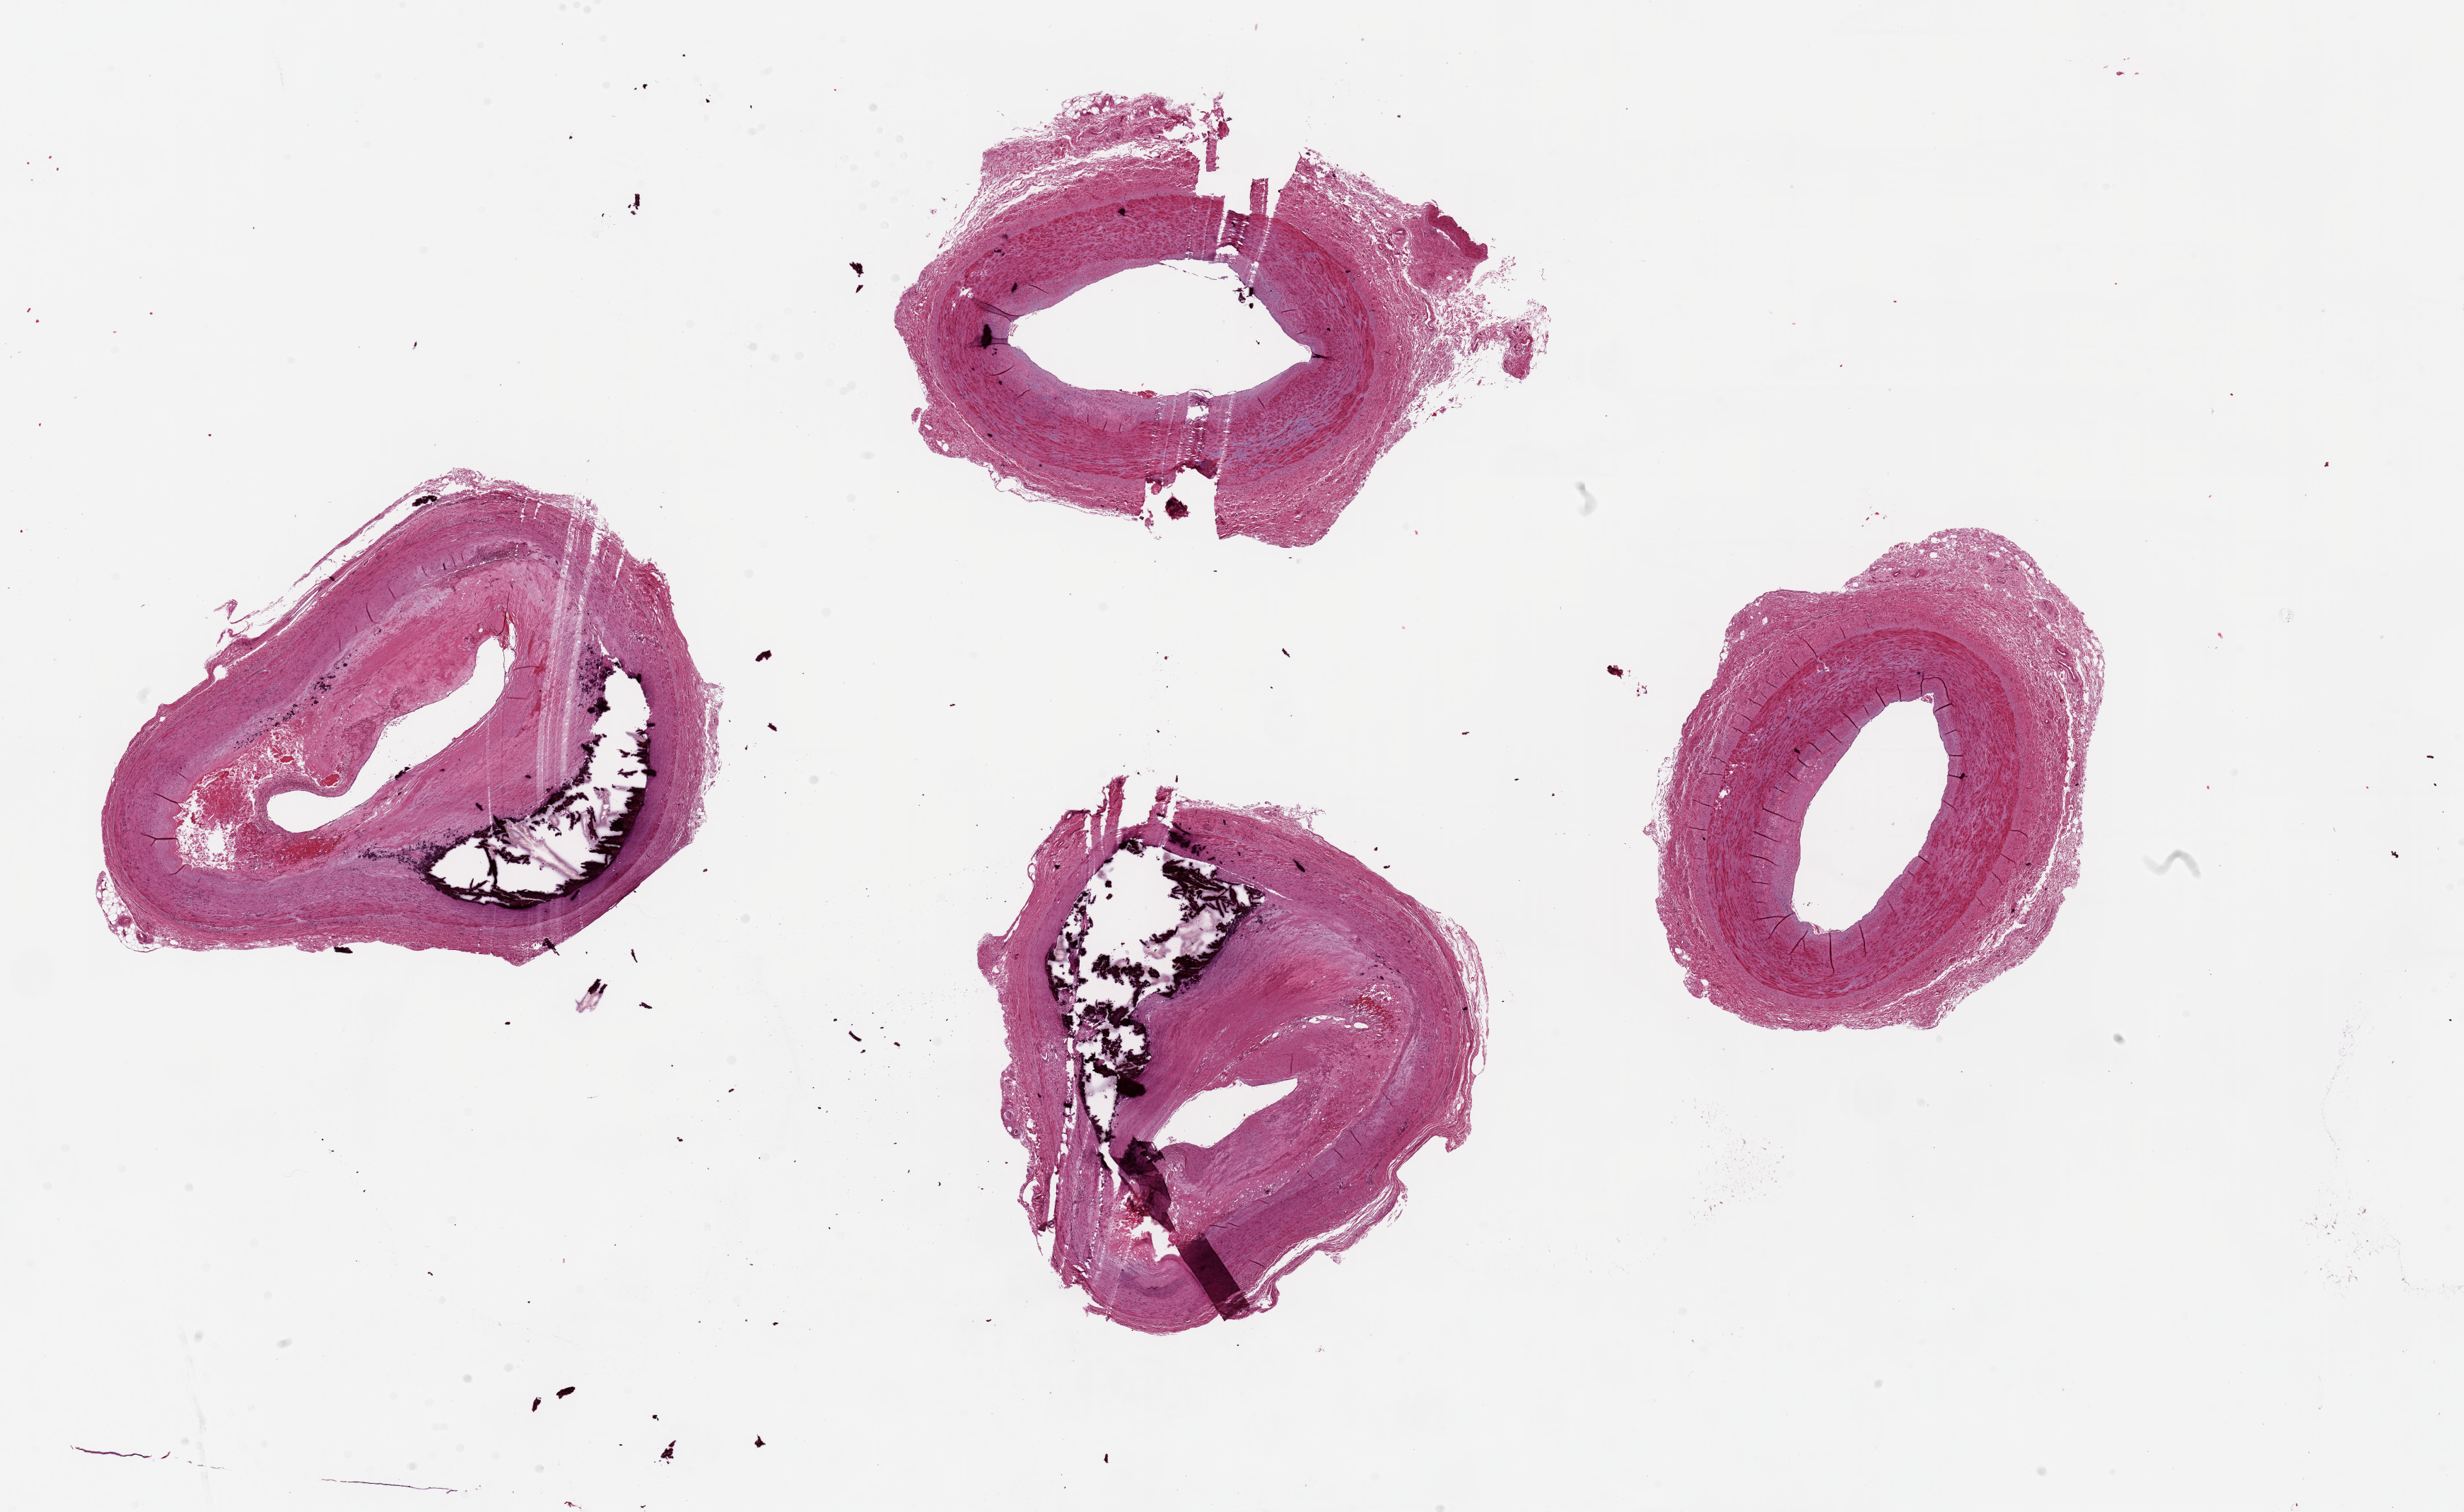
Digitized hematoxylin and eosin (H&E)-stained section, a low-resolution overview of the entire scanned area, about 27.6 x 16.9 mm (slide scanned at 20x). PAXgene-fixed, paraffin-embedded tissue. Section of tibial artery (target tissue). Donor tissue sample. Female donor.
Reviewer comment on this tissue sample: 4 pieces, up to 7x5mm; prominent calcfied atherosclerosis, good clean specimens.